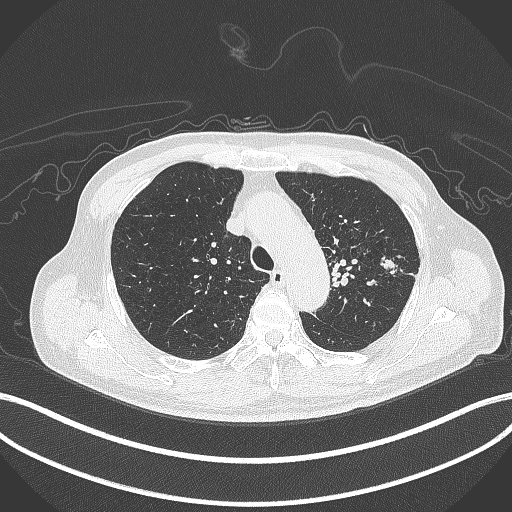
Chest CT, one axial slice. Slice 330 of 417 in the series (ordered by position). Lung window (W 1500 / L -600 HU). 1 mm slice thickness. 512 × 512 image matrix. Male patient, age 77 years. Case-level facts recorded for this patient, not image findings: clinical TNM (as recorded): T3 N1 M0.
Structures marked on this image (bounding box drawn by a radiologist):
- lung tumour (recorded histology: adenocarcinoma): bounding box (x1, y1, x2, y2) in pixels: (380, 253, 398, 275)